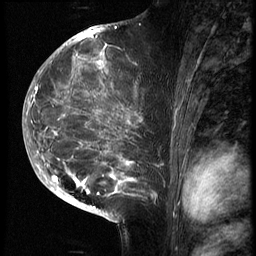
Breast MRI (dynamic contrast-enhanced), one sagittal slice. Position 35 of 70 along the scan axis. 3 images stored at this slice position (order not interpretable as contrast timing). 1.5 T. TE 4.2 ms, TR 9 ms. 2.5 mm slice thickness. 256 × 256 image matrix. Patient: female, 28 years. Case-level facts recorded for this patient, not image findings: setting: breast cancer imaged before/during neoadjuvant chemotherapy.
Structures marked on this image (semi-automatically segmented with operator editing):
- analysis volume of interest (the breast-tissue region the enhancement analysis was run in; not a lesion): box from (x=43, y=42) to (x=164, y=215) px
- tumour enhancement mask (voxels above the 140 % enhancement threshold inside the analysis volume of interest): (x=43, y=45)–(x=157, y=197)